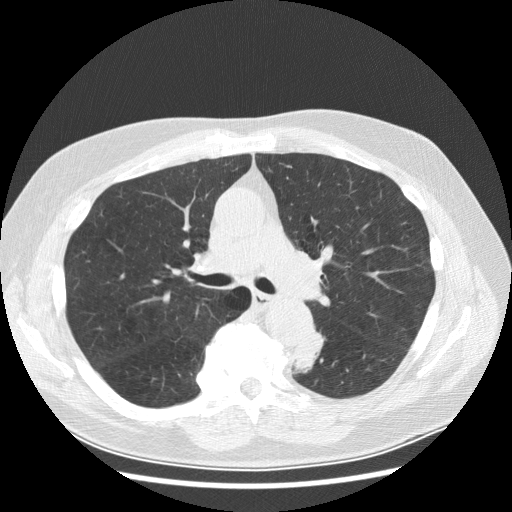
Chest CT (low-dose screening protocol), one axial image. Baseline screening round. Lung window (W 1500 / L -600 HU). Male participant, aged 70 years at enrolment. Current smoker at enrolment.
Lesion marked by an expert reader, bounding box <278,330,329,382> (left, top, right, bottom; pixels). Reader record for this screening exam (exam-level; its link to the box is not recorded): non-calcified nodule or mass ≥4 mm, left lower lobe, 27 × 16 mm, spiculated (stellate) margins, soft tissue attenuation, pre-existing on the prior screen: yes; interval growth: yes. Official screen result: positive, change unspecified: nodule(s) >= 4 mm or enlarging nodule(s), mass(es), or other non-specific abnormalities suspicious for lung cancer. Participant outcome: lung cancer diagnosed 97 days after this screen — papillary adenocarcinoma, NOS, left lower lobe, moderately differentiated (G2), stage IB (AJCC 6th edition), 35 mm at pathology.